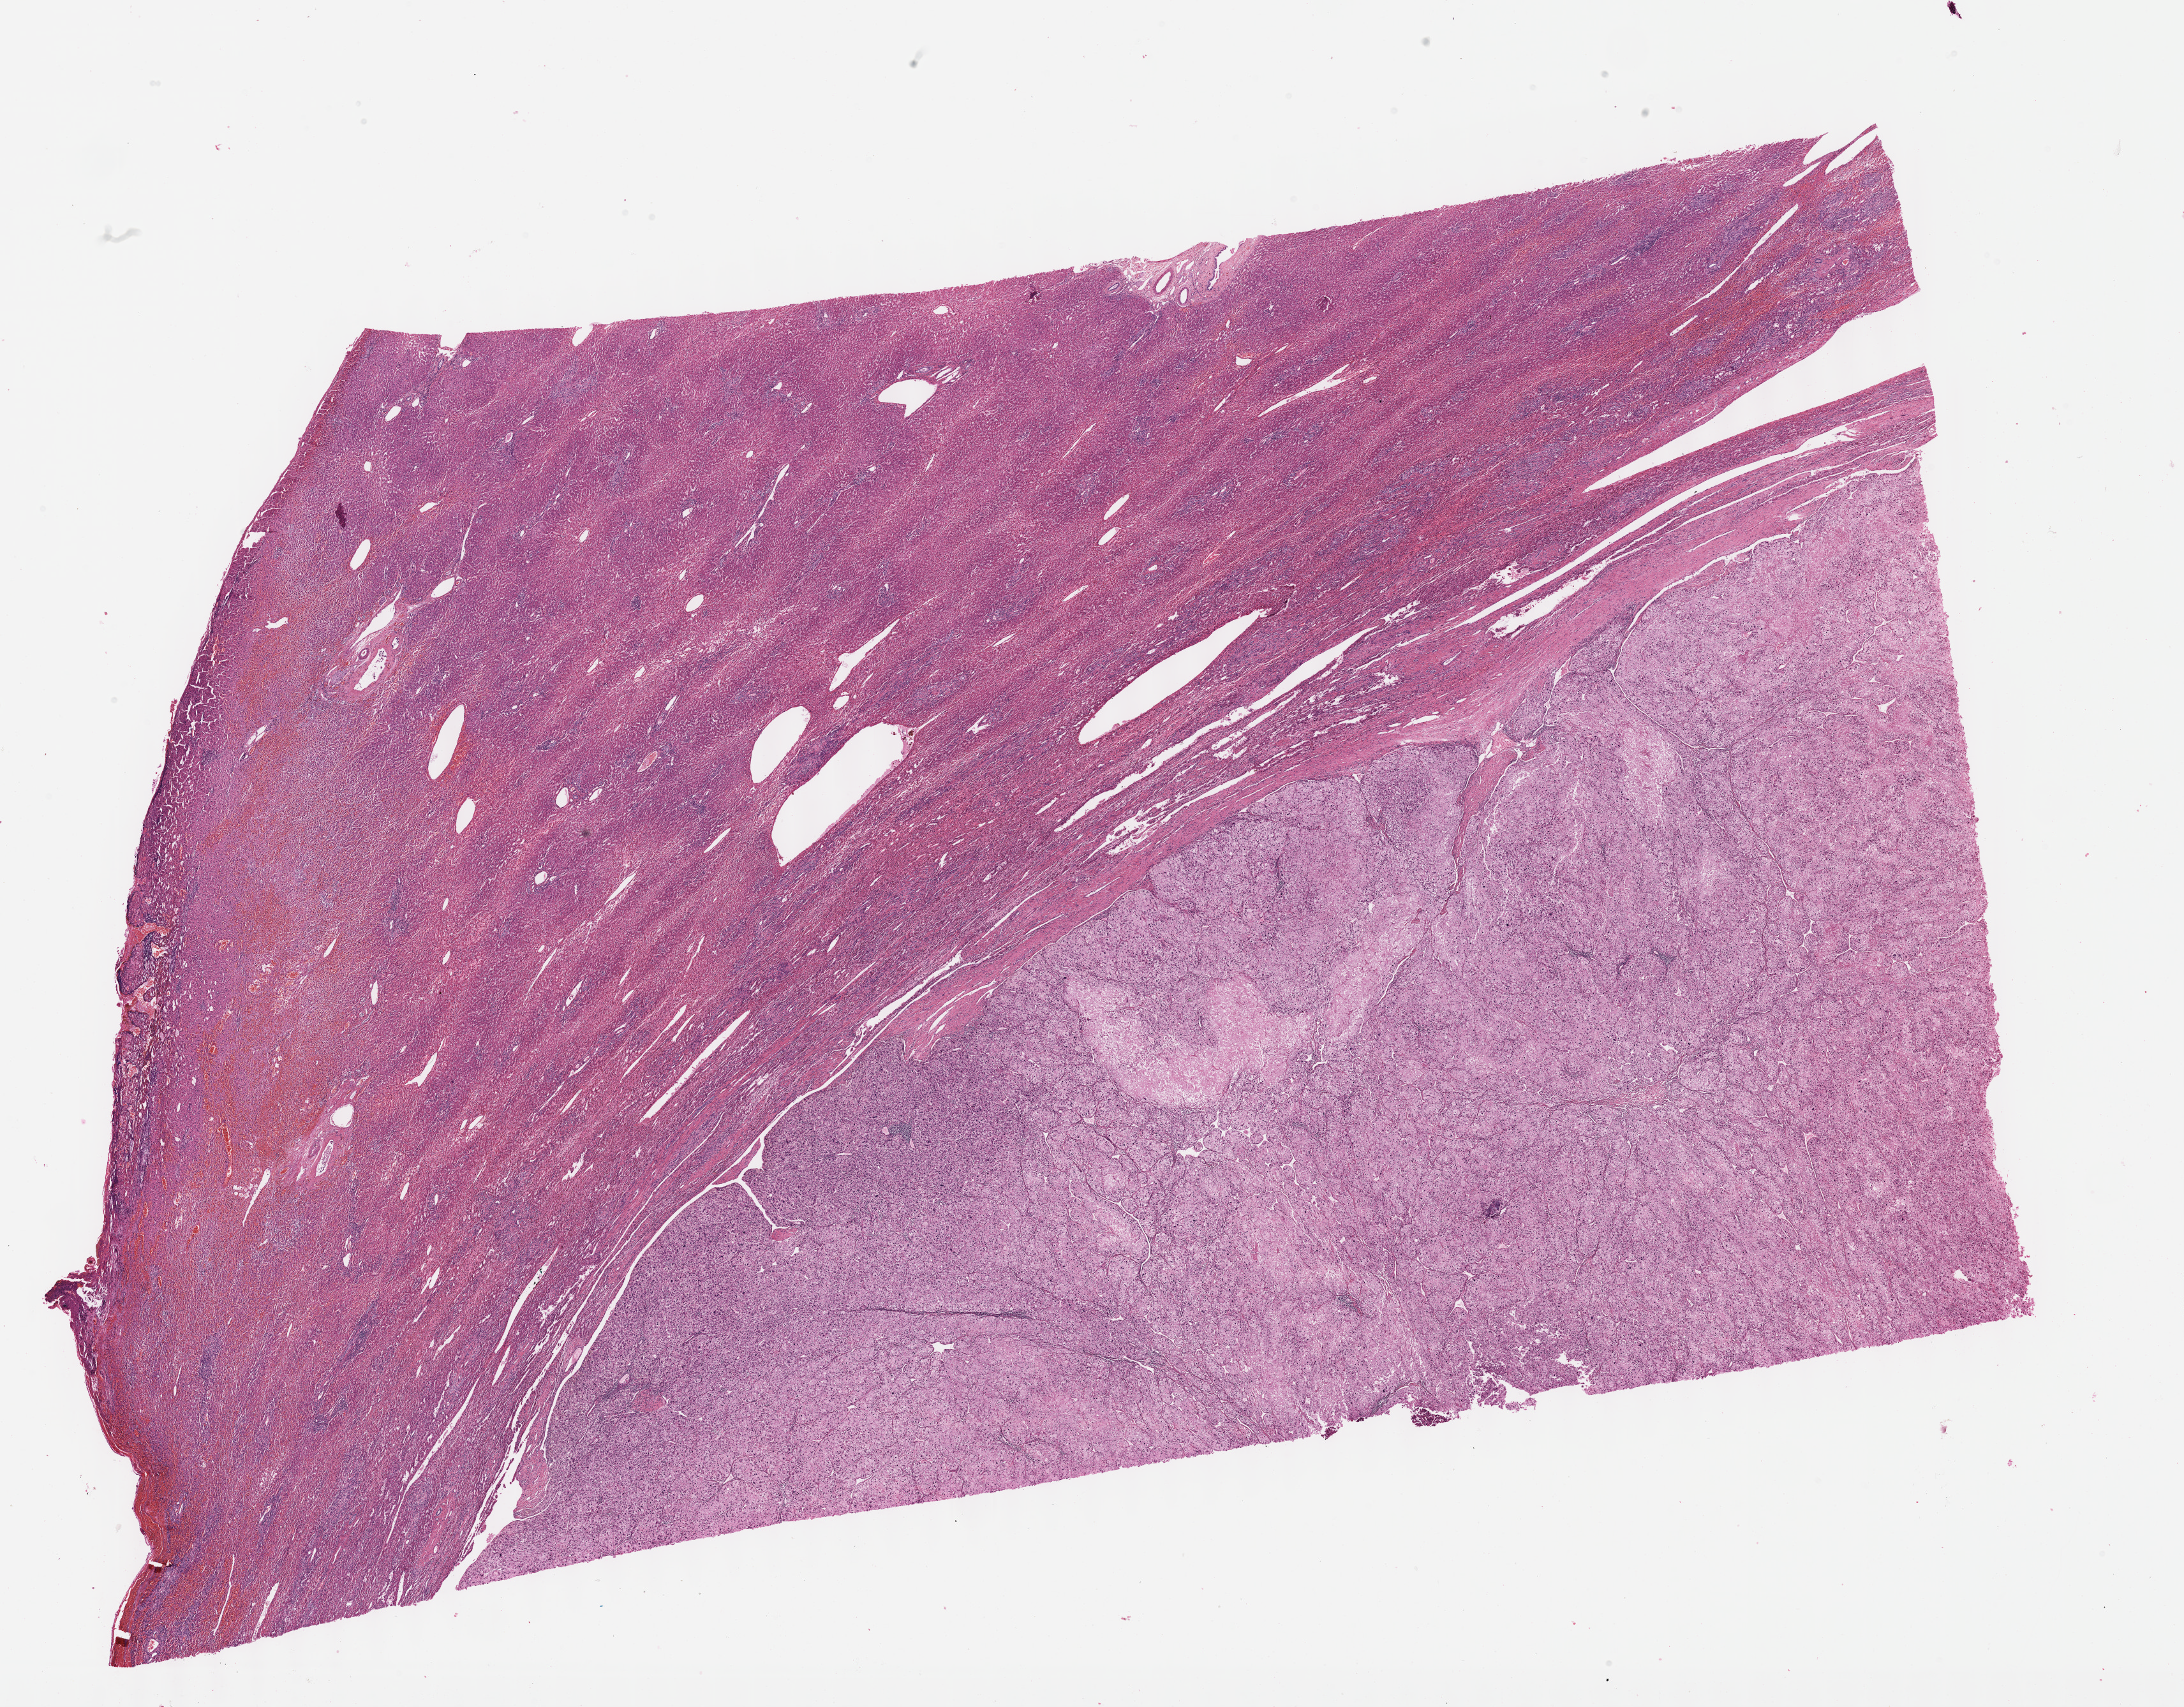
Whole-slide histology image, H&E-stained, whole scanned area (about 27.7 x 21.6 mm, slide scanned at 40x) shown as a low-resolution overview. FFPE section. Liver, primary tumour sample. Patient: female, age at initial diagnosis 49 years. Histologic grade: G3 (poorly differentiated).
- pathologic diagnosis: Hepatocellular carcinoma, clear cell type
- TNM: T3 N0 M0
- AJCC pathologic stage: IIIB (7th edition)